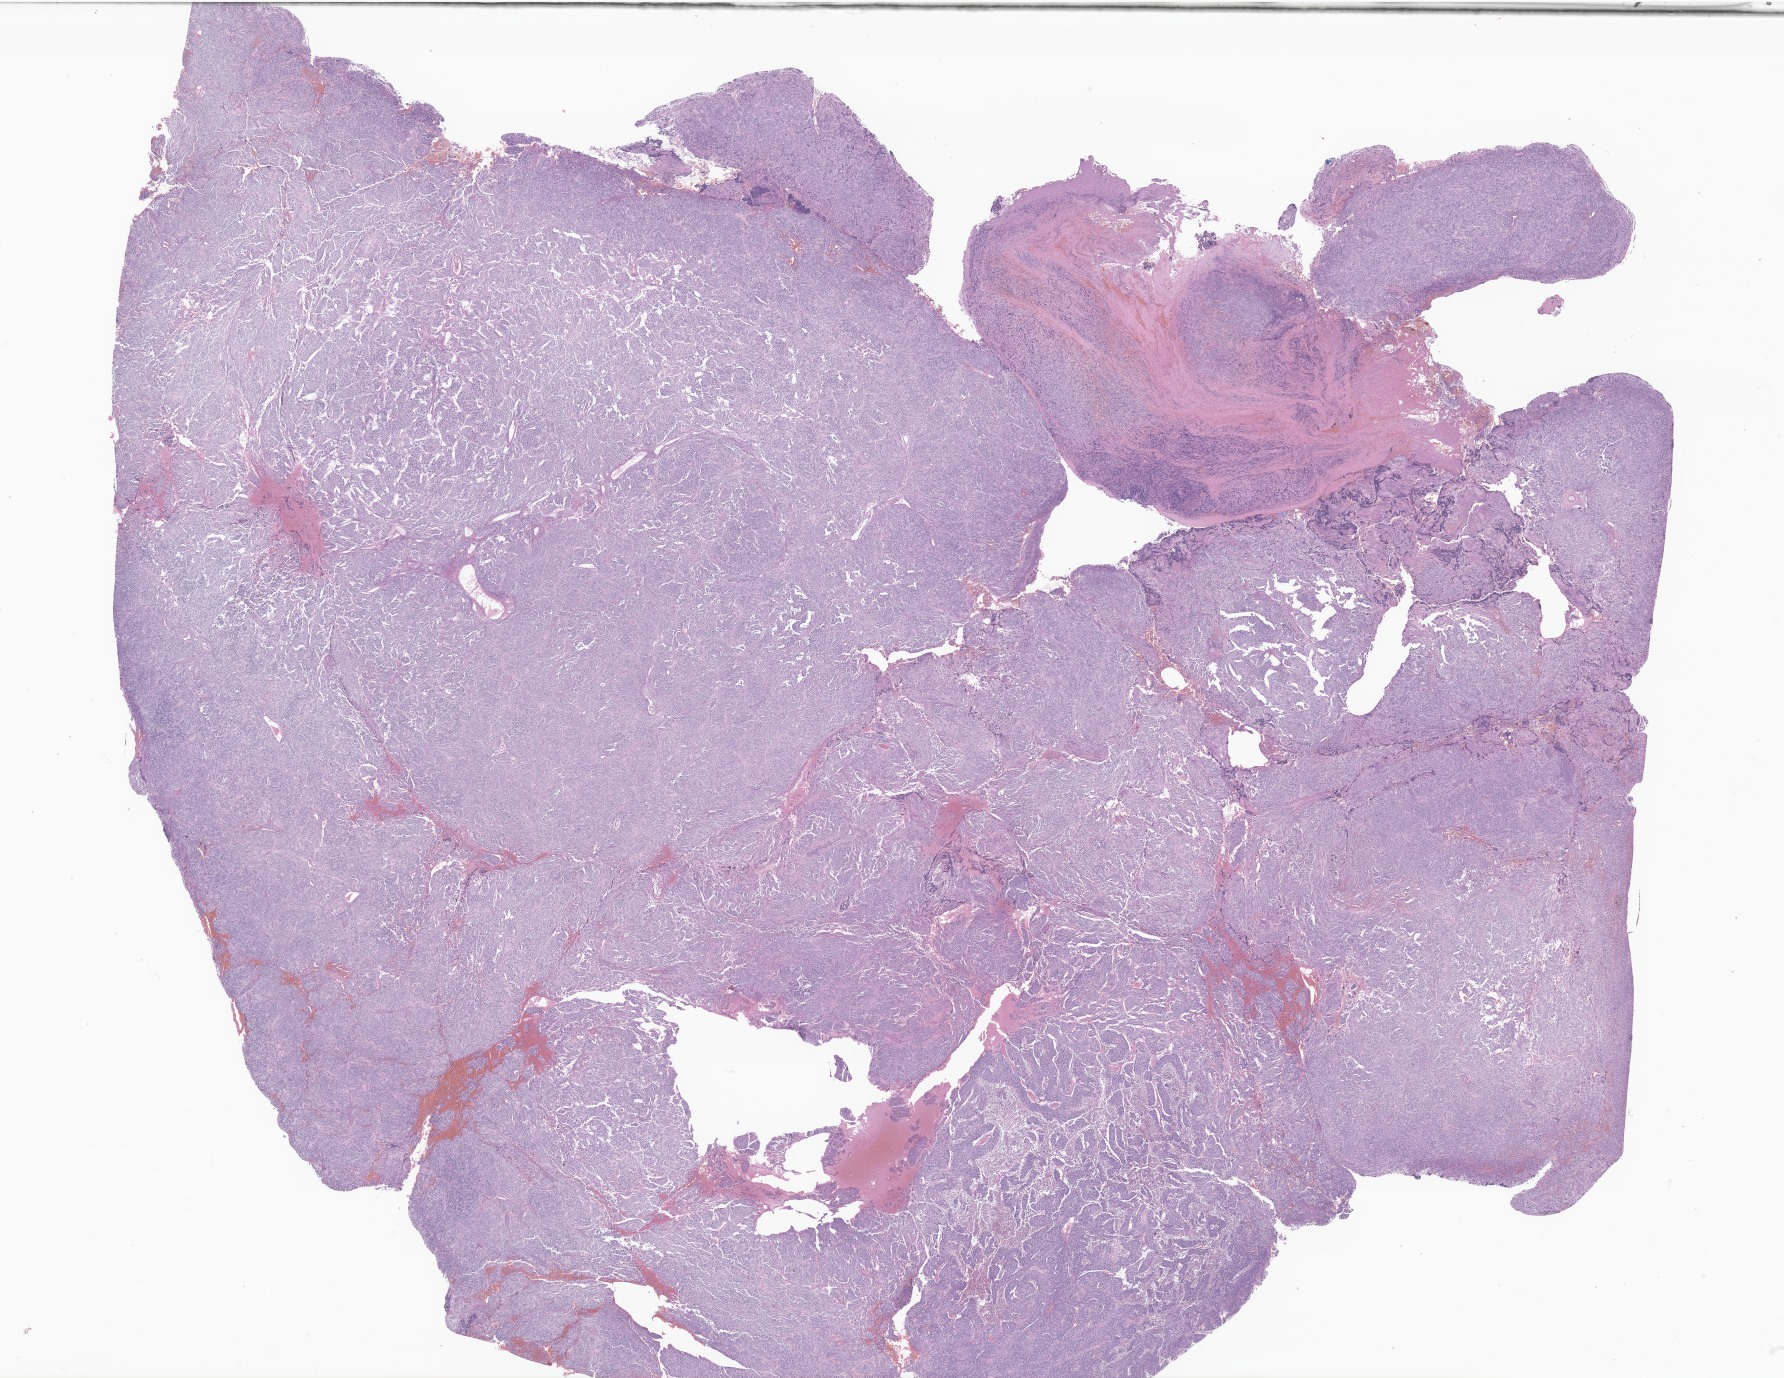
H&E whole-slide image of tumor tissue from the posterior mediastinum — a low-resolution overview of the entire scanned area, about 30.1 x 23.2 mm, formalin-fixed paraffin-embedded section. Male patient, age 50 days.
Recorded diagnosis: Neuroblastoma, NOS.